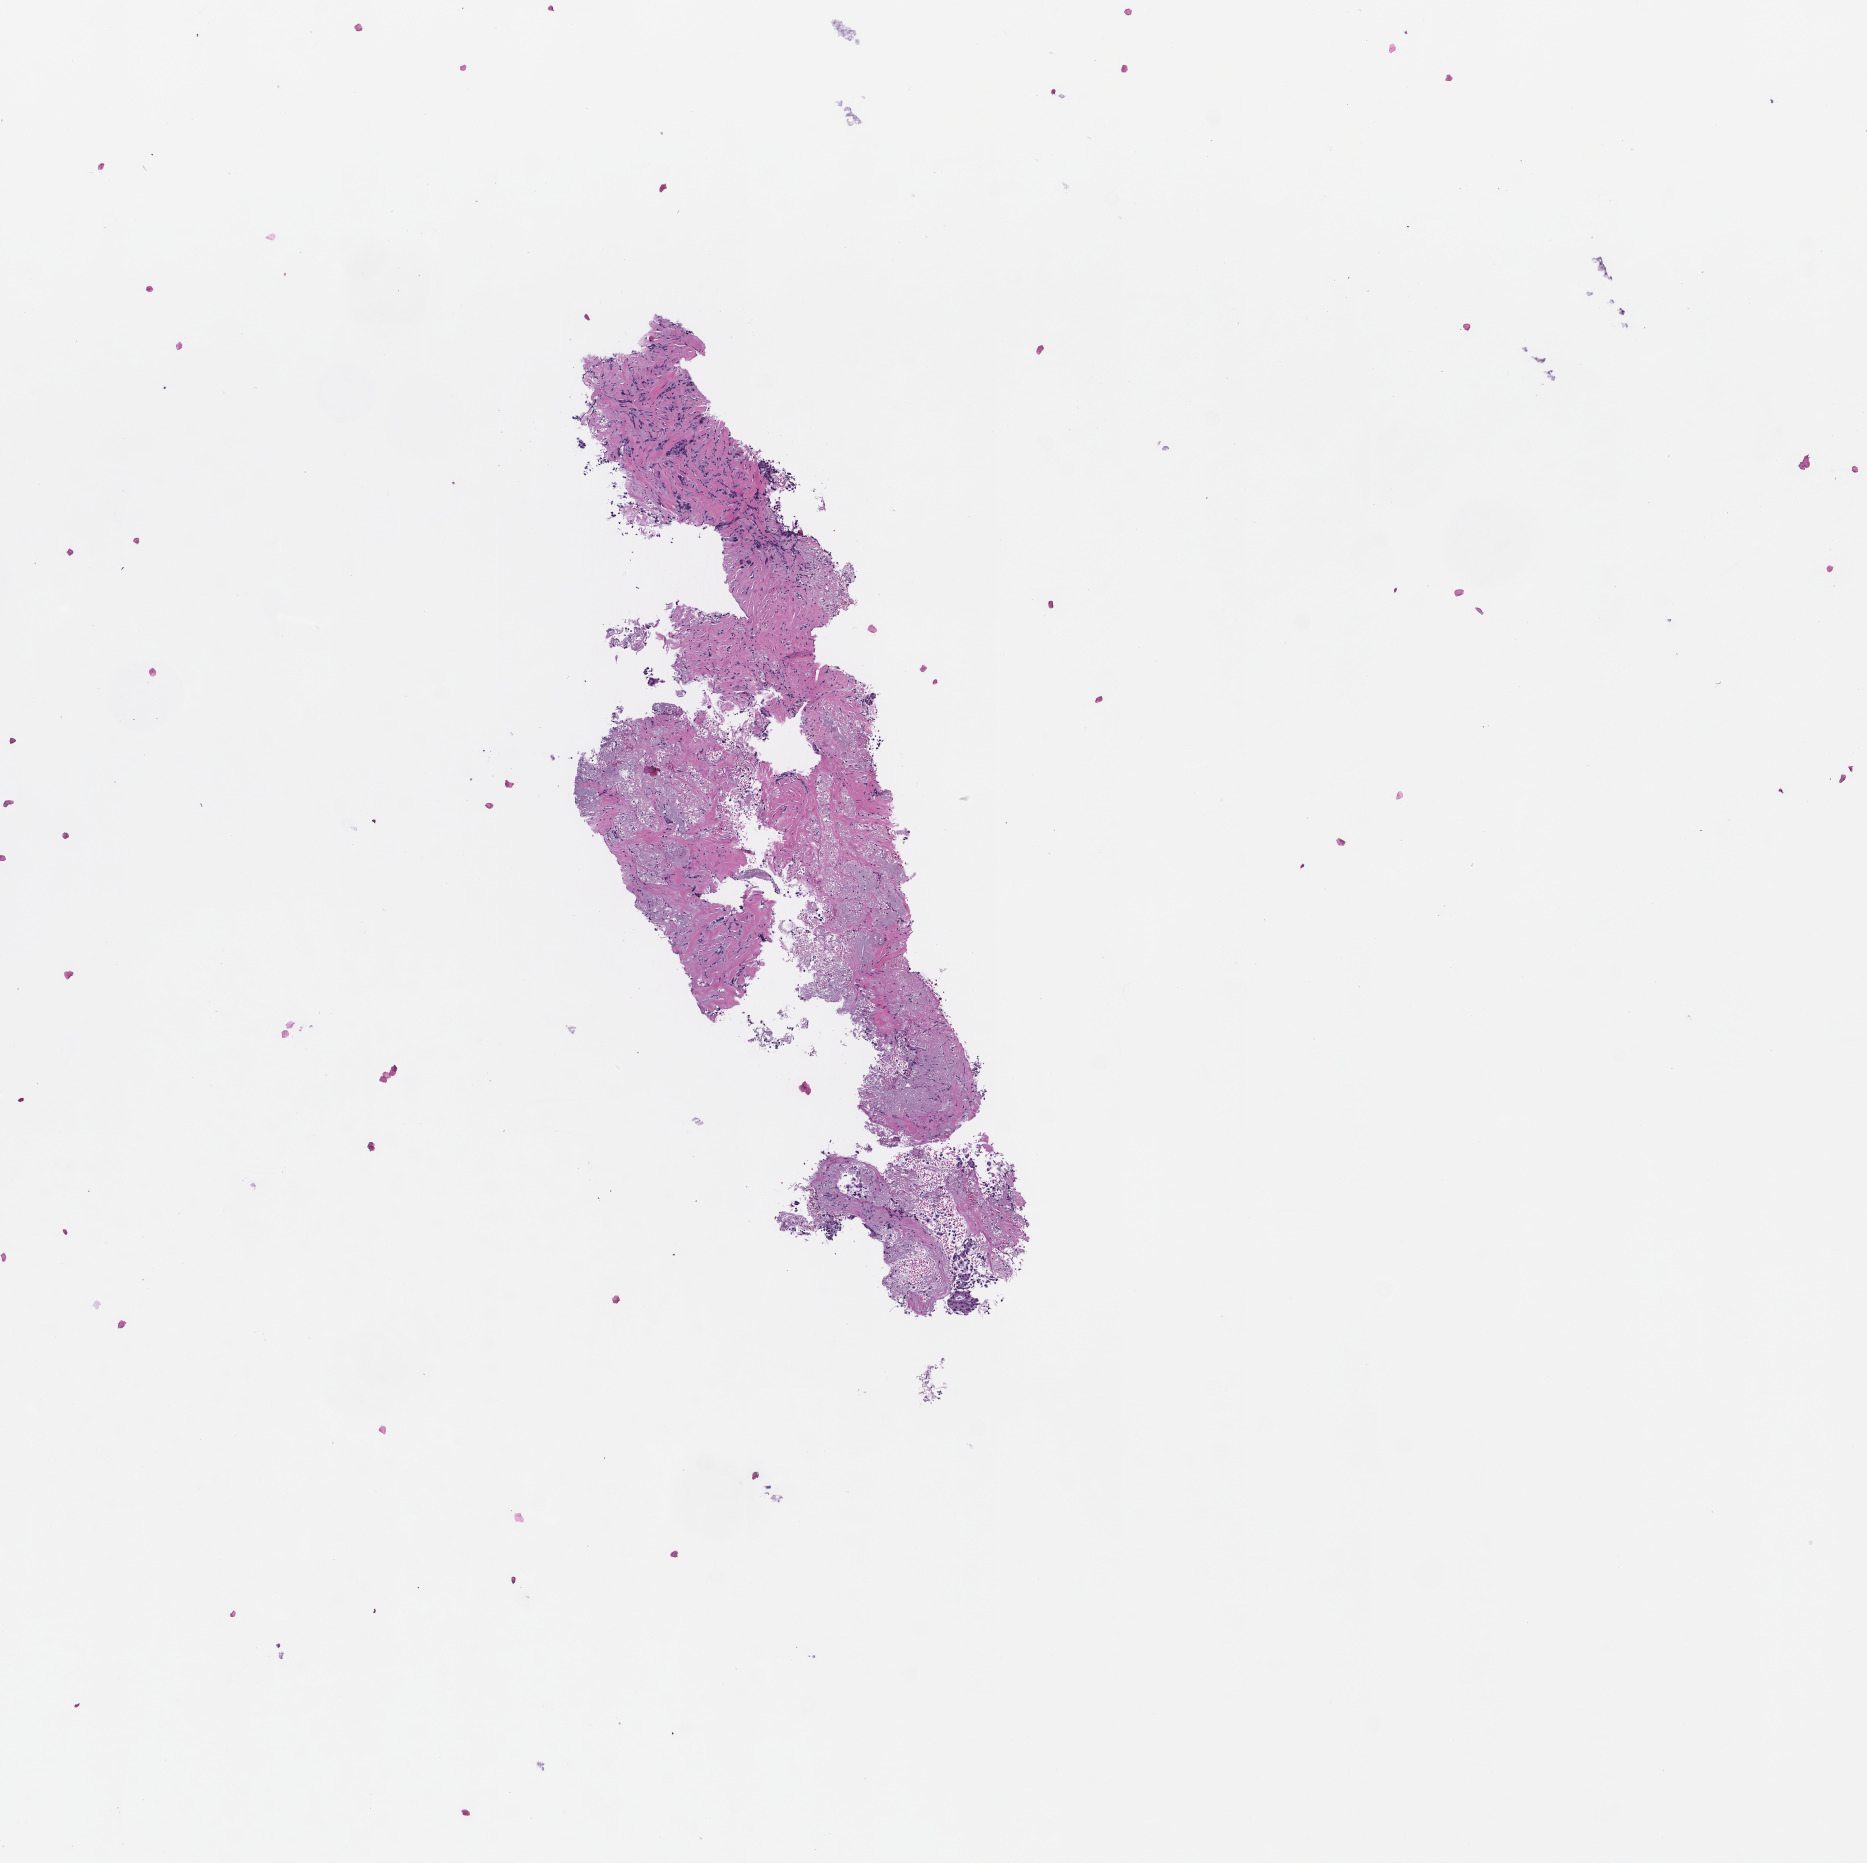
Digitized haematoxylin and eosin-stained section, whole scanned area (about 7.5 x 7.5 mm) shown as a low-resolution overview, formalin-fixed, paraffin-embedded (FFPE) tissue, tissue site: breast, collected at baseline (before treatment). Patient sex: female.
This section: primary tumour tissue. Diagnosis: Invasive Breast Carcinoma.